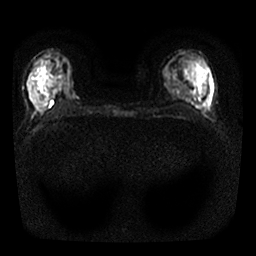
Breast MRI, one axial slice; slice 9 of 25 in the series (ordered by position); diffusion-weighted series; image 2 of 4 stored at this slice position (different b-values; order by instance number); 1.5 T; 4 mm slice thickness; 256 × 256 image matrix, field of view 300 × 300 mm. Female patient.
Outlined on this slice (outlined manually by an expert reader):
- tumour on diffusion-weighted imaging: bounding box [x1, y1, x2, y2] px = [52, 90, 56, 97]